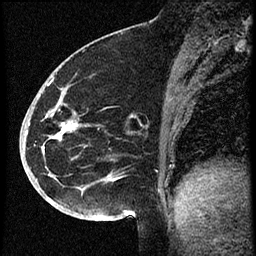
Breast MRI (dynamic contrast-enhanced), one sagittal slice. Slice 28 of 60 in the series (ordered by position). Dynamic contrast-enhanced study with each time point stored as its own series, time point 2 of 3 at this slice position (early post-contrast, ordered by acquisition time). 1.5 T. TE 4.2 ms, TR 18.9 ms. 256 × 256 image matrix. Female patient. From the clinical record (not read from this slice): setting: breast cancer imaged before/during neoadjuvant chemotherapy; receptor status: HR-positive, HER2-negative.
Outlined on this slice (semi-automatic segmentation, software-assisted and operator-edited):
- analysis volume of interest (the breast-tissue region the enhancement analysis was run in; not a lesion): bounding box <30,87,114,173> (left, top, right, bottom; pixels)
- tumour enhancement mask (voxels above the 100 % enhancement threshold inside the analysis volume of interest): <55,122,78,140>